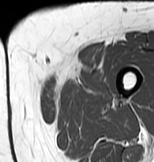
MRI of an extremity soft-tissue mass, one axial slice; position 9 of 83 along the scan axis; MR volume resampled by the dataset authors to the PET/CT grid (not the native acquisition matrix); 3.27 mm slice thickness; 154 × 162 image matrix, field of view 150 × 158 mm. Female patient. Case-level facts recorded for this patient, not image findings: histological type: myxofibrosarcoma; grade: intermediate; site of the primary tumour: left thigh.
Annotated regions visible in this slice (expert contour drawn on MRI and transferred to this co-registered scan by the dataset authors):
- gross tumour volume including surrounding oedema: box from (x=42, y=63) to (x=111, y=103) px